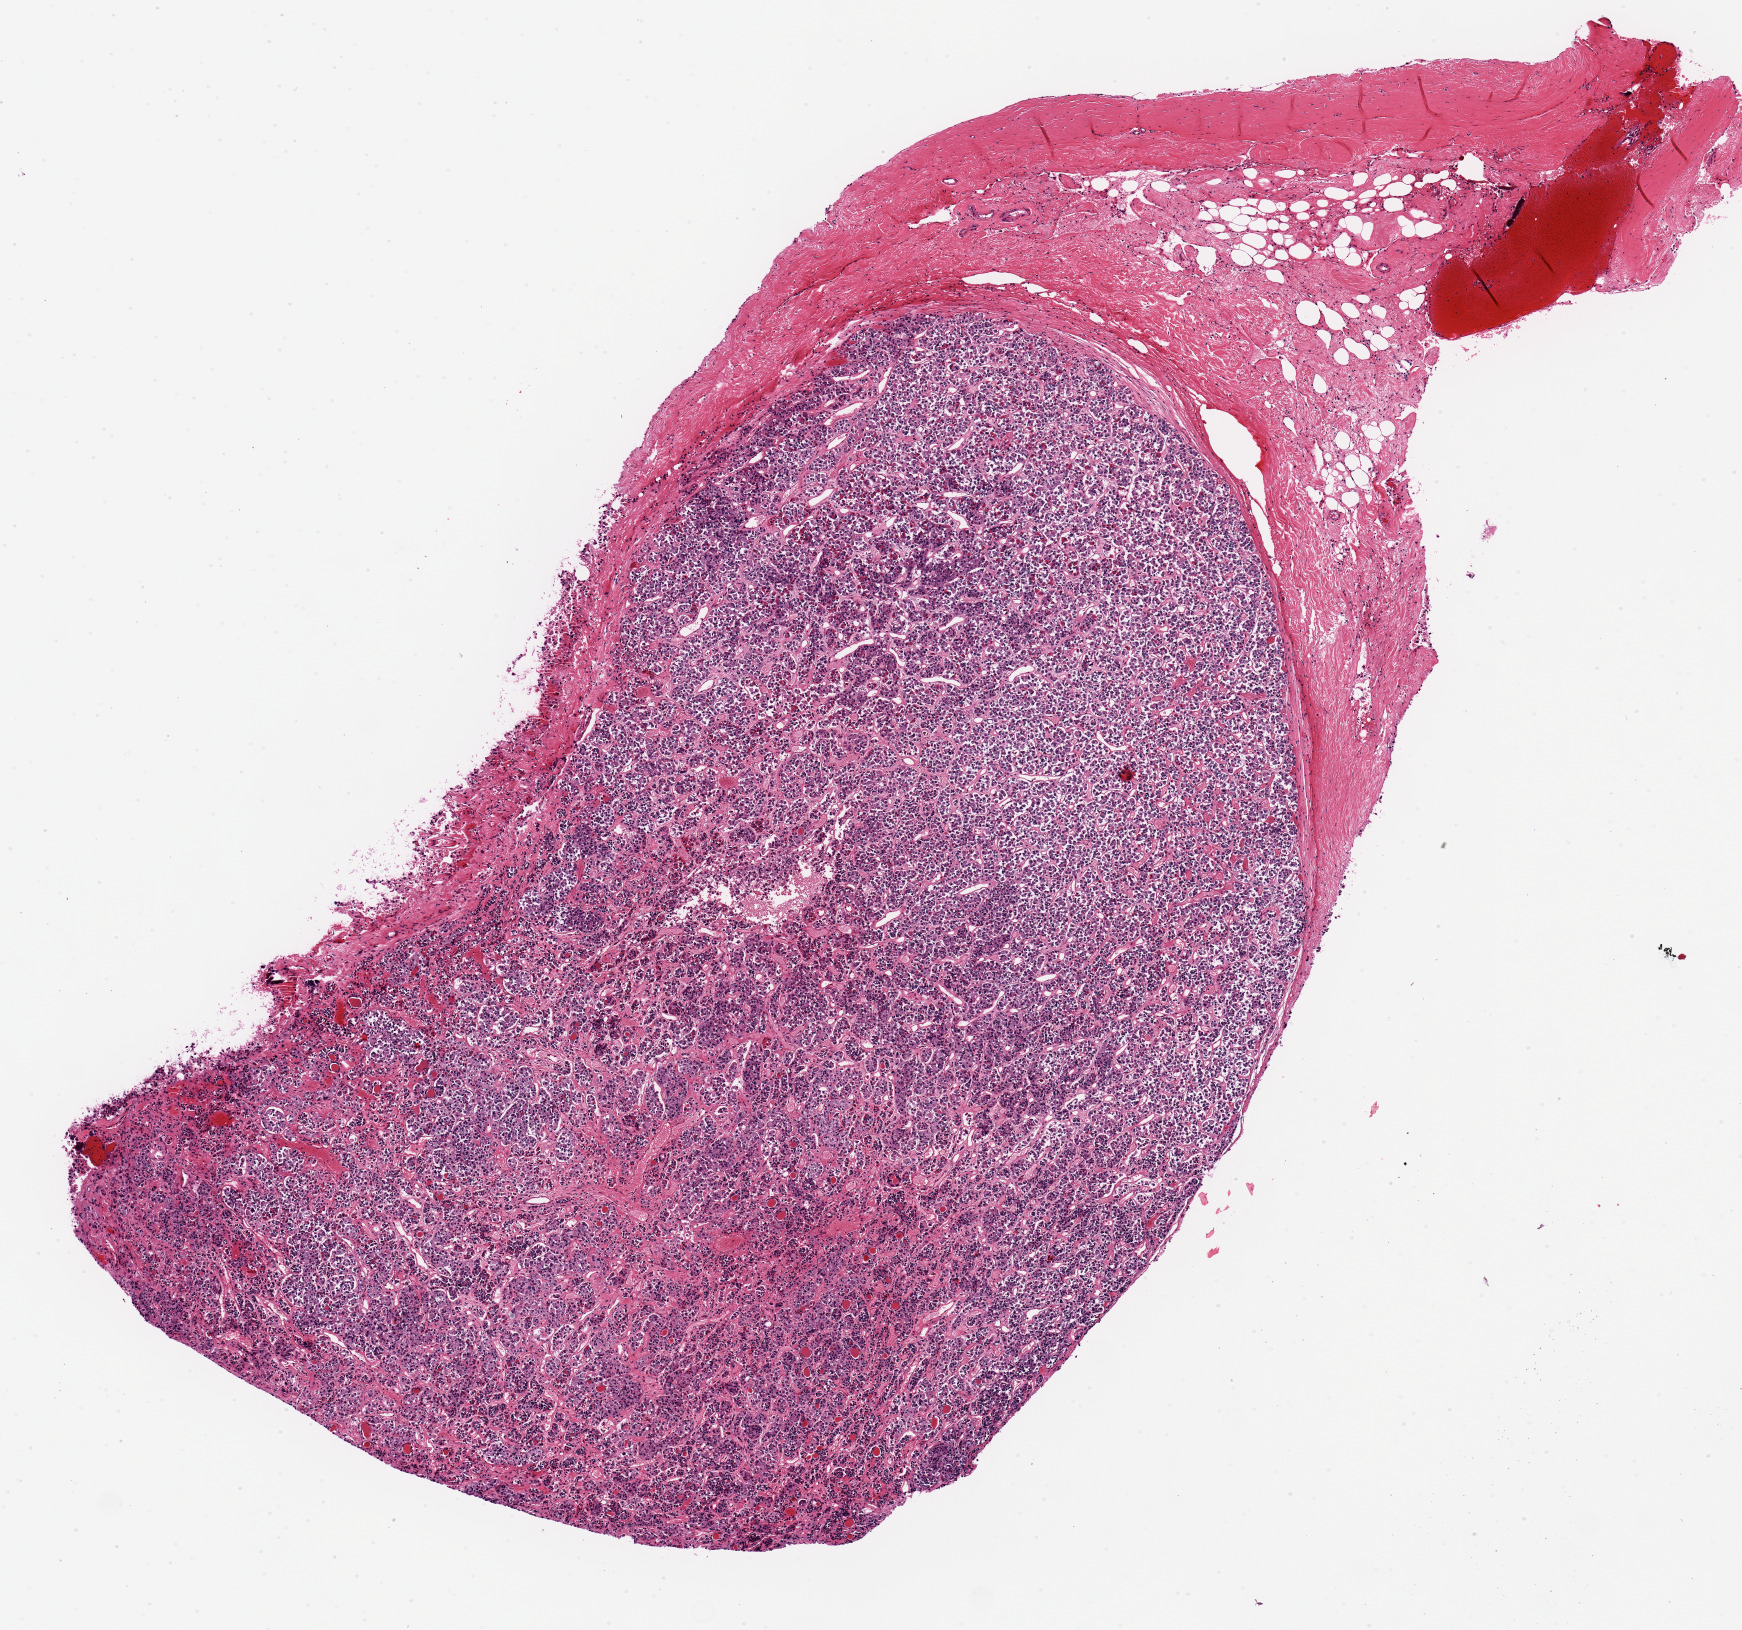
Digitized hematoxylin and eosin (H&E)-stained section, low-resolution overview of the scanned area, about 6.9 x 6.4 mm (slide scanned at 20x), PAXgene-fixed, paraffin-embedded tissue, sampled site (target tissue): pituitary, donor tissue sample. Donor: male.
Reviewer comment on this tissue sample: 1 piece 7x3 mm; anterior.